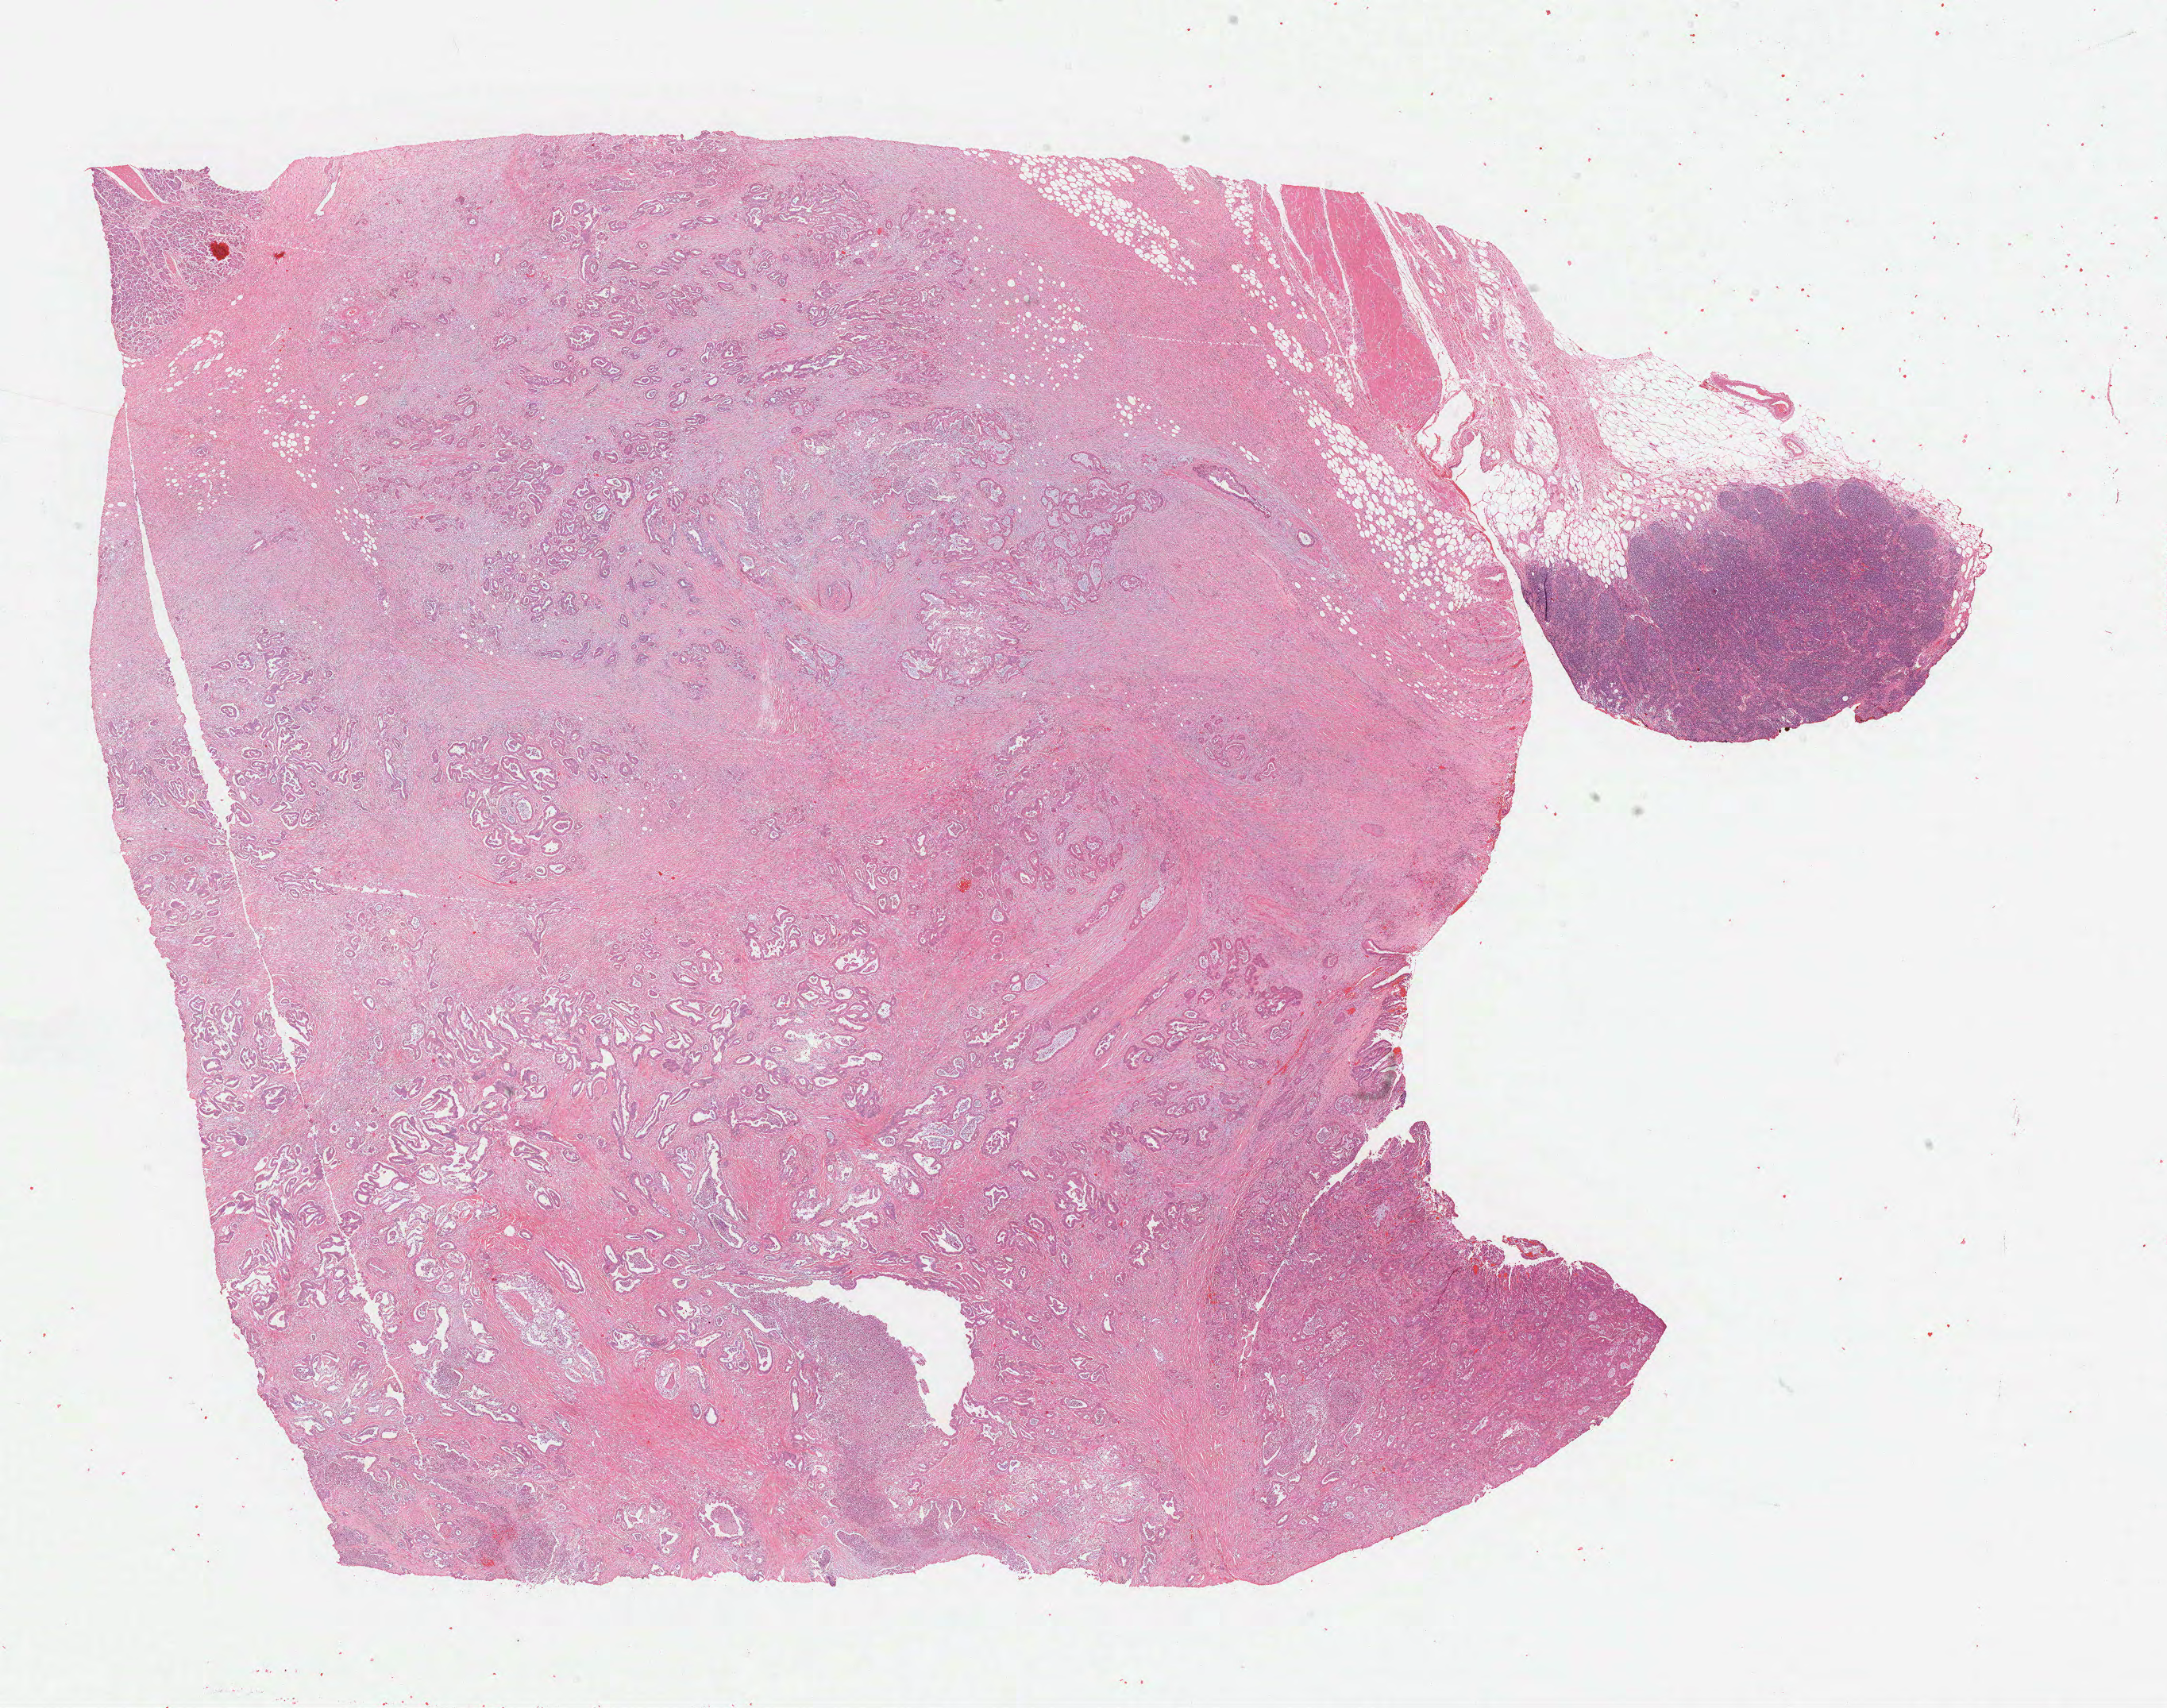
Whole-slide histology image, H&E-stained, whole scanned area (about 22.0 x 17.4 mm, acquisition: 40x scan) shown as a low-resolution overview; formalin-fixed paraffin-embedded (FFPE) diagnostic section; pancreas, primary tumour sample. Patient: male, age at initial diagnosis 47 years. Histologic grade: G2 (moderately differentiated).
Lymph nodes positive (case pathology): 3 of 21 examined. AJCC pathologic stage: IIB. Histologic diagnosis: Infiltrating duct carcinoma, NOS (head of pancreas).